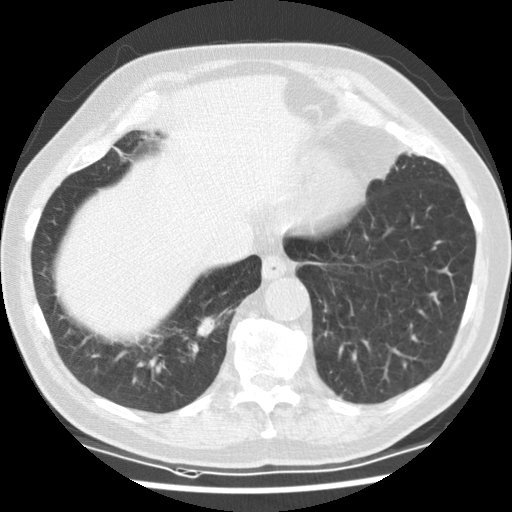
Low-dose screening chest CT, one axial slice; slice 24 of 135 in the series (ordered by position); reconstruction kernel STANDARD; 120 kVp; lung window (W 1500 / L -600 HU); 2.5 mm slice thickness; 512 × 512 image matrix, field of view 340 × 340 mm.
Structures marked on this image (expert manual segmentation):
- lesion 2 (nodule, upper lobe of right lung): bounding box <197,315,221,337> (left, top, right, bottom; pixels)